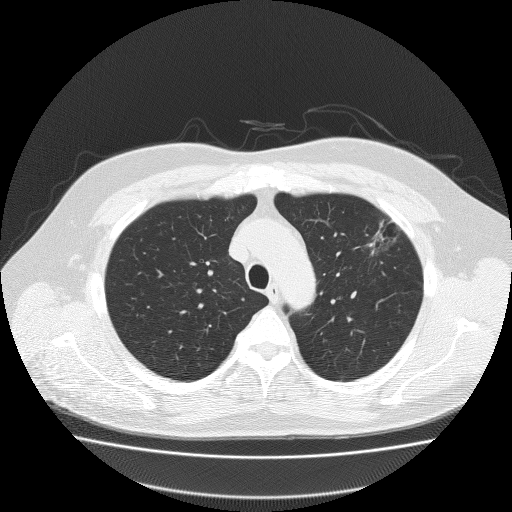
Low-dose screening chest CT, one axial slice. Position 156 of 204 along the scan axis. Lung window (W 1500 / L -600 HU). 2 mm slice thickness. 512 × 512 image matrix, field of view 410 × 410 mm.
Annotated regions visible in this slice (expert manual segmentation):
- lesion 1 (tumor, upper lobe of left lung): box from (x=367, y=228) to (x=394, y=256) px